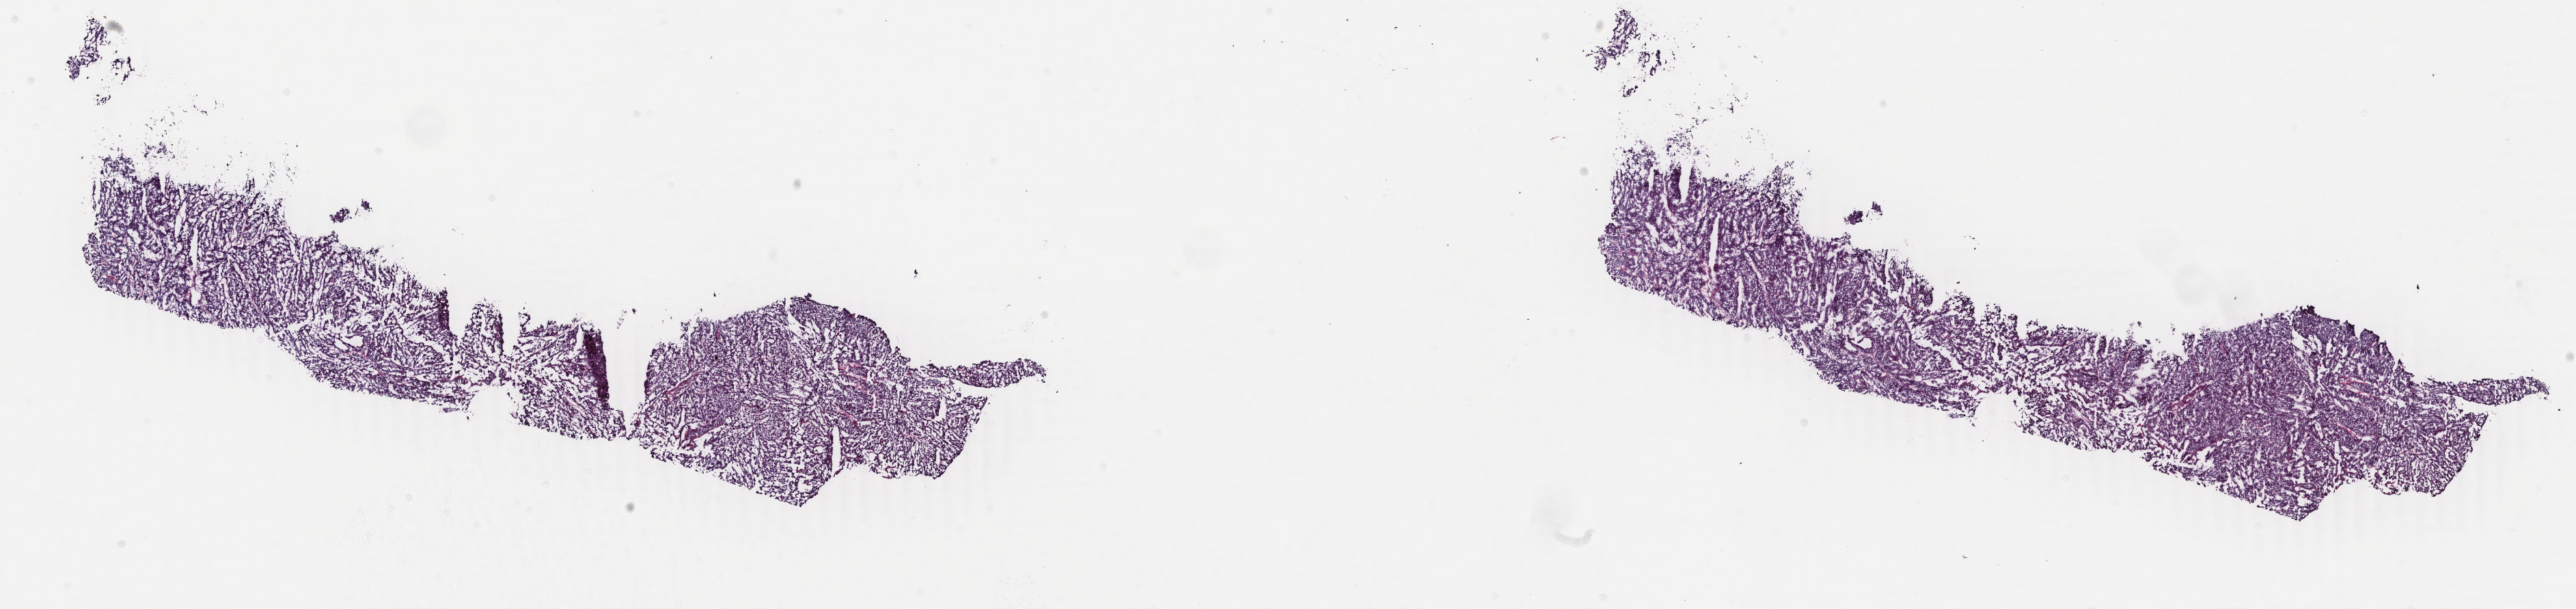
Digitized H&E tissue section (whole slide), whole scanned area (about 30.0 x 7.1 mm) shown as a low-resolution overview; frozen section from the top of the tissue portion; sample: primary tumour, uterus. Patient sex: female. Histologic grade: G2 (moderately differentiated). Slide review estimates, as recorded: tumour cells 70%, tumour nuclei 70%, normal cells 0%, stromal cells 25%, necrosis 5%. Inflammatory infiltration, as recorded: lymphocyte infiltration 30%, monocyte infiltration 20%, neutrophil infiltration 40%.
* FIGO stage: II
* pathologic diagnosis: Endometrioid adenocarcinoma, NOS (endometrium)